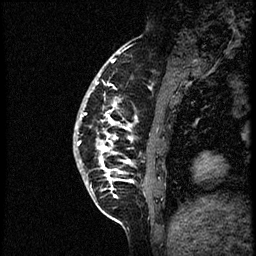
Breast MRI (dynamic contrast-enhanced), one sagittal slice; slice 15 of 56 in the series (ordered by position); dynamic contrast-enhanced study with each time point stored as its own series, time point 2 of 3 at this slice position (early post-contrast, ordered by acquisition time); 1.5 T; TE 4.2 ms, TR 21.3 ms; 2 mm slice thickness; 256 × 256 image matrix, field of view 200 × 200 mm. Patient: female, 41 years. Case-level facts recorded for this patient, not image findings: setting: breast cancer imaged before/during neoadjuvant chemotherapy; receptor status: HER2-positive.
Structures marked on this image (semi-automatic segmentation, software-assisted and operator-edited):
- analysis volume of interest (the breast-tissue region the enhancement analysis was run in; not a lesion): bounding box [x1, y1, x2, y2] px = [73, 73, 177, 205]
- tumour enhancement mask (voxels above the 100 % enhancement threshold inside the analysis volume of interest): [78, 80, 136, 188]